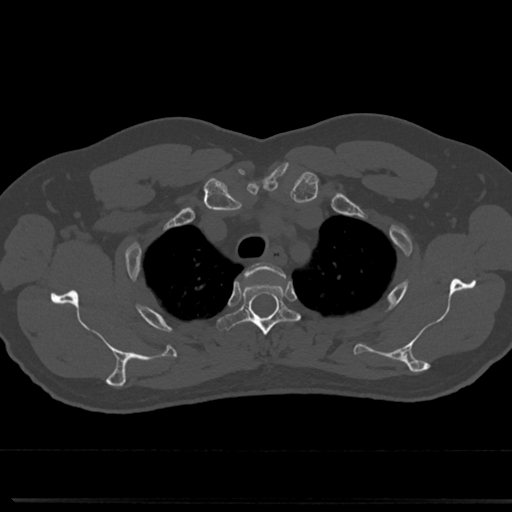
CT including the spine, one axial slice. Slice 599 of 817 in the series (ordered by position). Reconstruction kernel Br40s/3. 120 kVp. Bone window (W 1800 / L 400 HU). 512 × 512 image matrix, field of view 355 × 355 mm. Patient: male, 61 years. From the clinical record (not read from this slice): primary cancer: prostate.
Structures marked on this image (semi-automatic segmentation, software-assisted and operator-edited):
- T2 vertebra: bounding box <272,266,276,269> (left, top, right, bottom; pixels)
- T3 vertebra: <225,267,295,344>